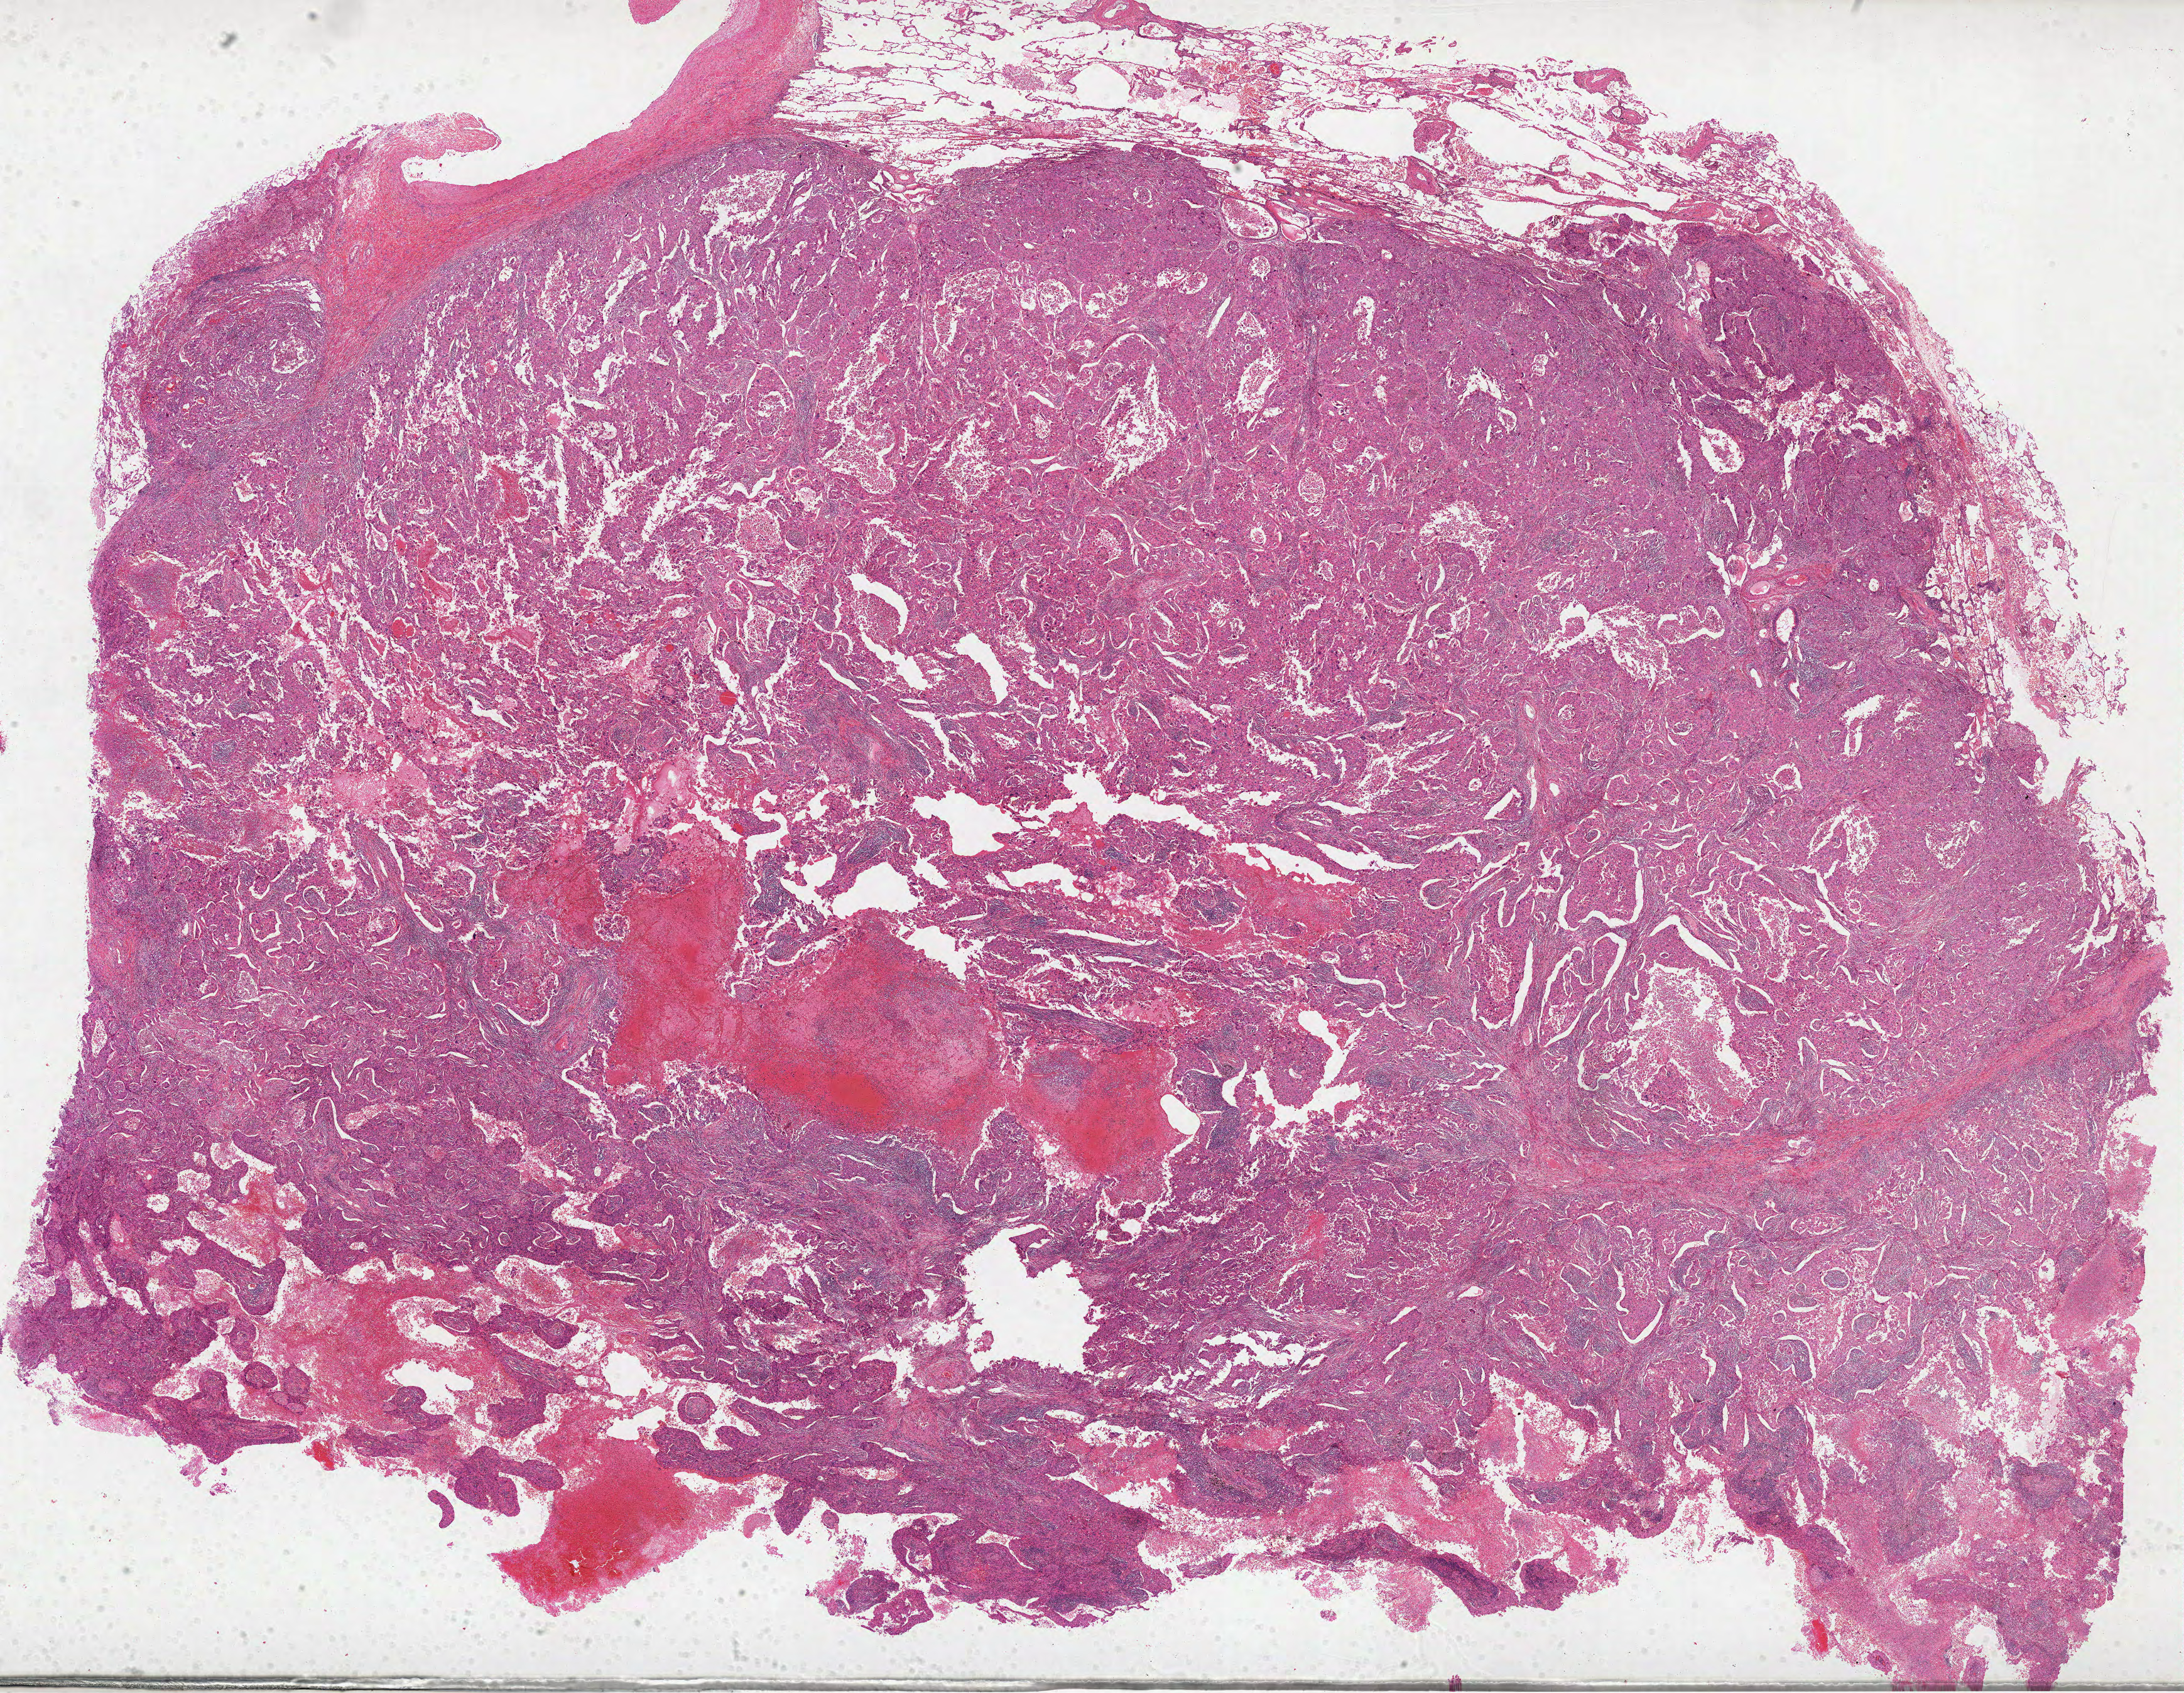
Whole-slide histology image, H&E, low-resolution overview of the scanned area, about 28.0 x 21.7 mm (slide scanned at 40x), formalin-fixed paraffin-embedded (FFPE) diagnostic section, primary tumour sample from the lung. Patient: male, age at initial diagnosis 68 years.
Diagnosis: Squamous cell carcinoma, NOS (upper lobe, lung). TNM: T2 N1 M0. Laterality: right. AJCC pathologic stage: IIB (6th edition).